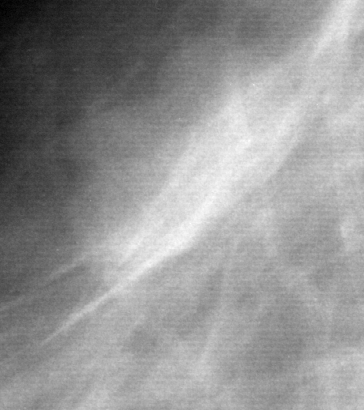
Crop from a digitized film mammogram around one marked abnormality, right breast, CC view.
Mass, shape lobulated, margins circumscribed; BI-RADS assessment category 3; pathology (as recorded): benign.